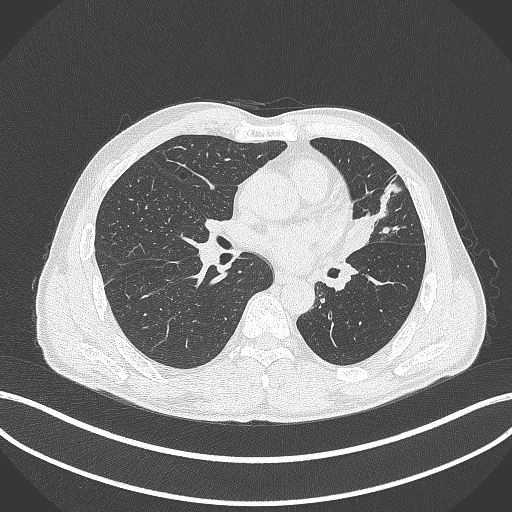
Chest CT, one axial slice. Slice 217 of 429 in the series (ordered by position). 120 kVp. Lung window (W 1500 / L -600 HU). 1 mm slice thickness. 512 × 512 image matrix, field of view 400 × 400 mm. Patient: male, 57 years. Case-level facts recorded for this patient, not image findings: clinical TNM (as recorded): T2b N0 M0.
Annotated regions visible in this slice (rectangle marked by the reading radiologist):
- lung tumour (recorded histology: squamous cell carcinoma): bounding box <337,205,375,268> (left, top, right, bottom; pixels)